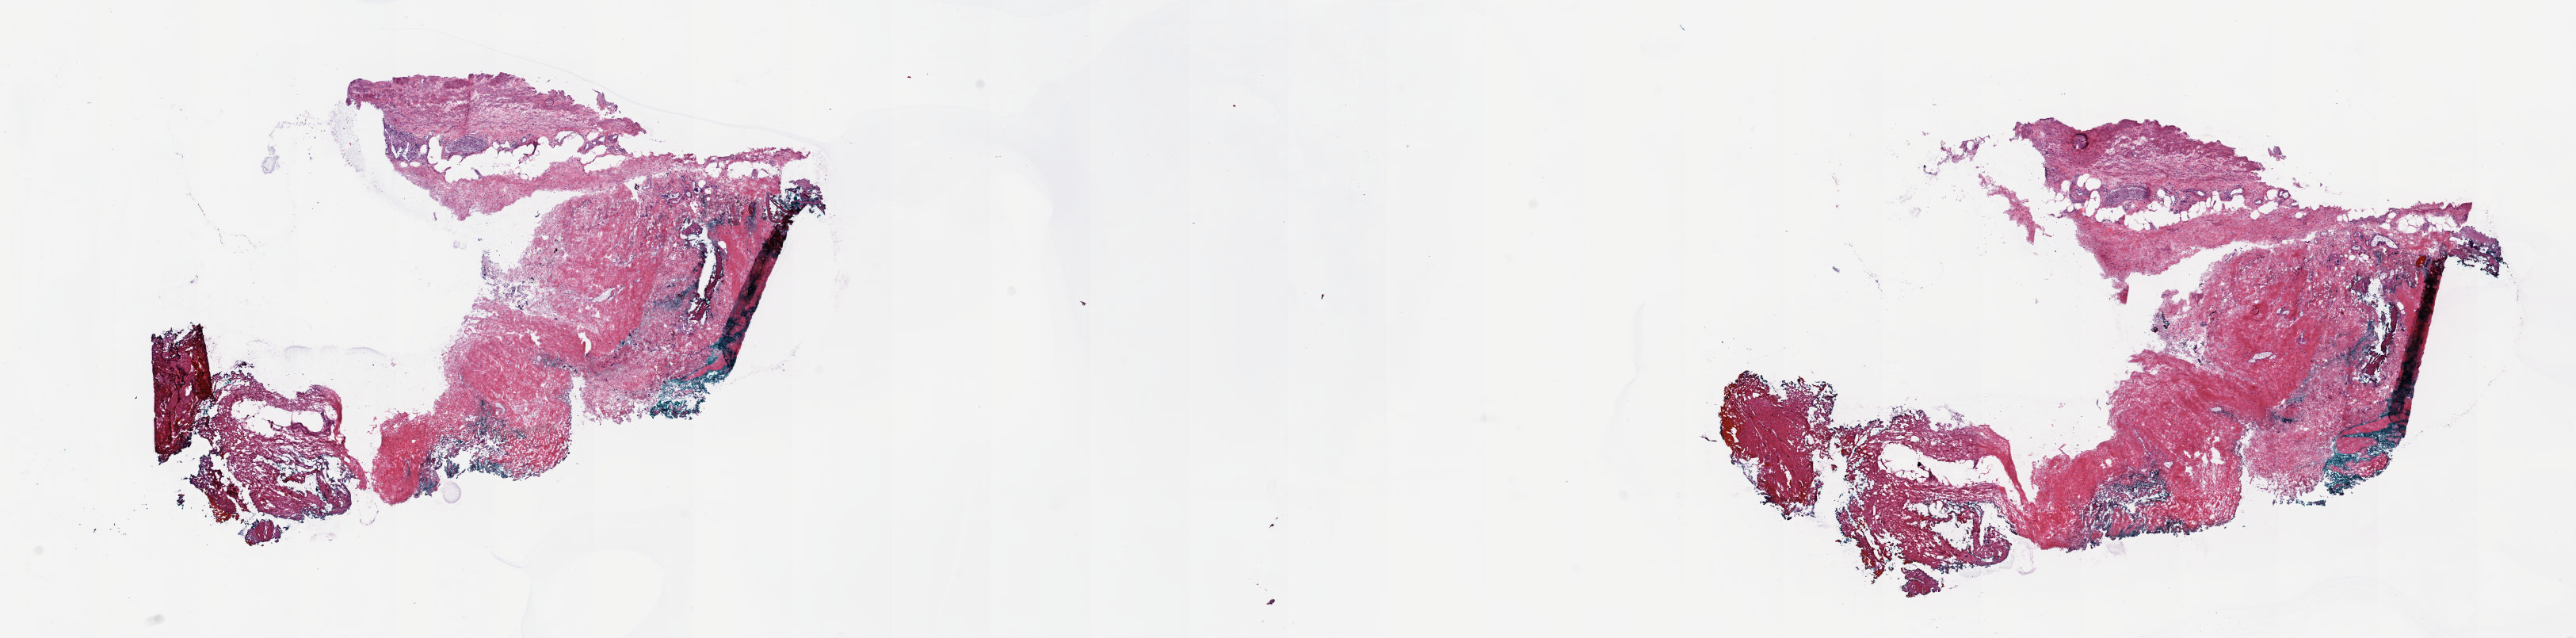
Hematoxylin and eosin (H&E) stained whole-slide image — whole scanned area (about 25.8 x 6.4 mm, slide scanned at 20x) shown as a low-resolution overview, frozen section from the top of the tissue portion, bladder, solid tissue normal (non-tumour tissue) sample. Male, age 63 years at initial diagnosis. Slide review estimates, as recorded: tumour cells 0%, tumour nuclei 0%, normal cells 100%, stromal cells 0%, necrosis 0%. Inflammatory infiltration, as recorded: lymphocyte infiltration 1%, monocyte infiltration 0%, neutrophil infiltration 0%.
• this section: solid tissue normal sample (biorepository sample class)
• patient diagnosis: Transitional cell carcinoma (posterior wall of bladder)